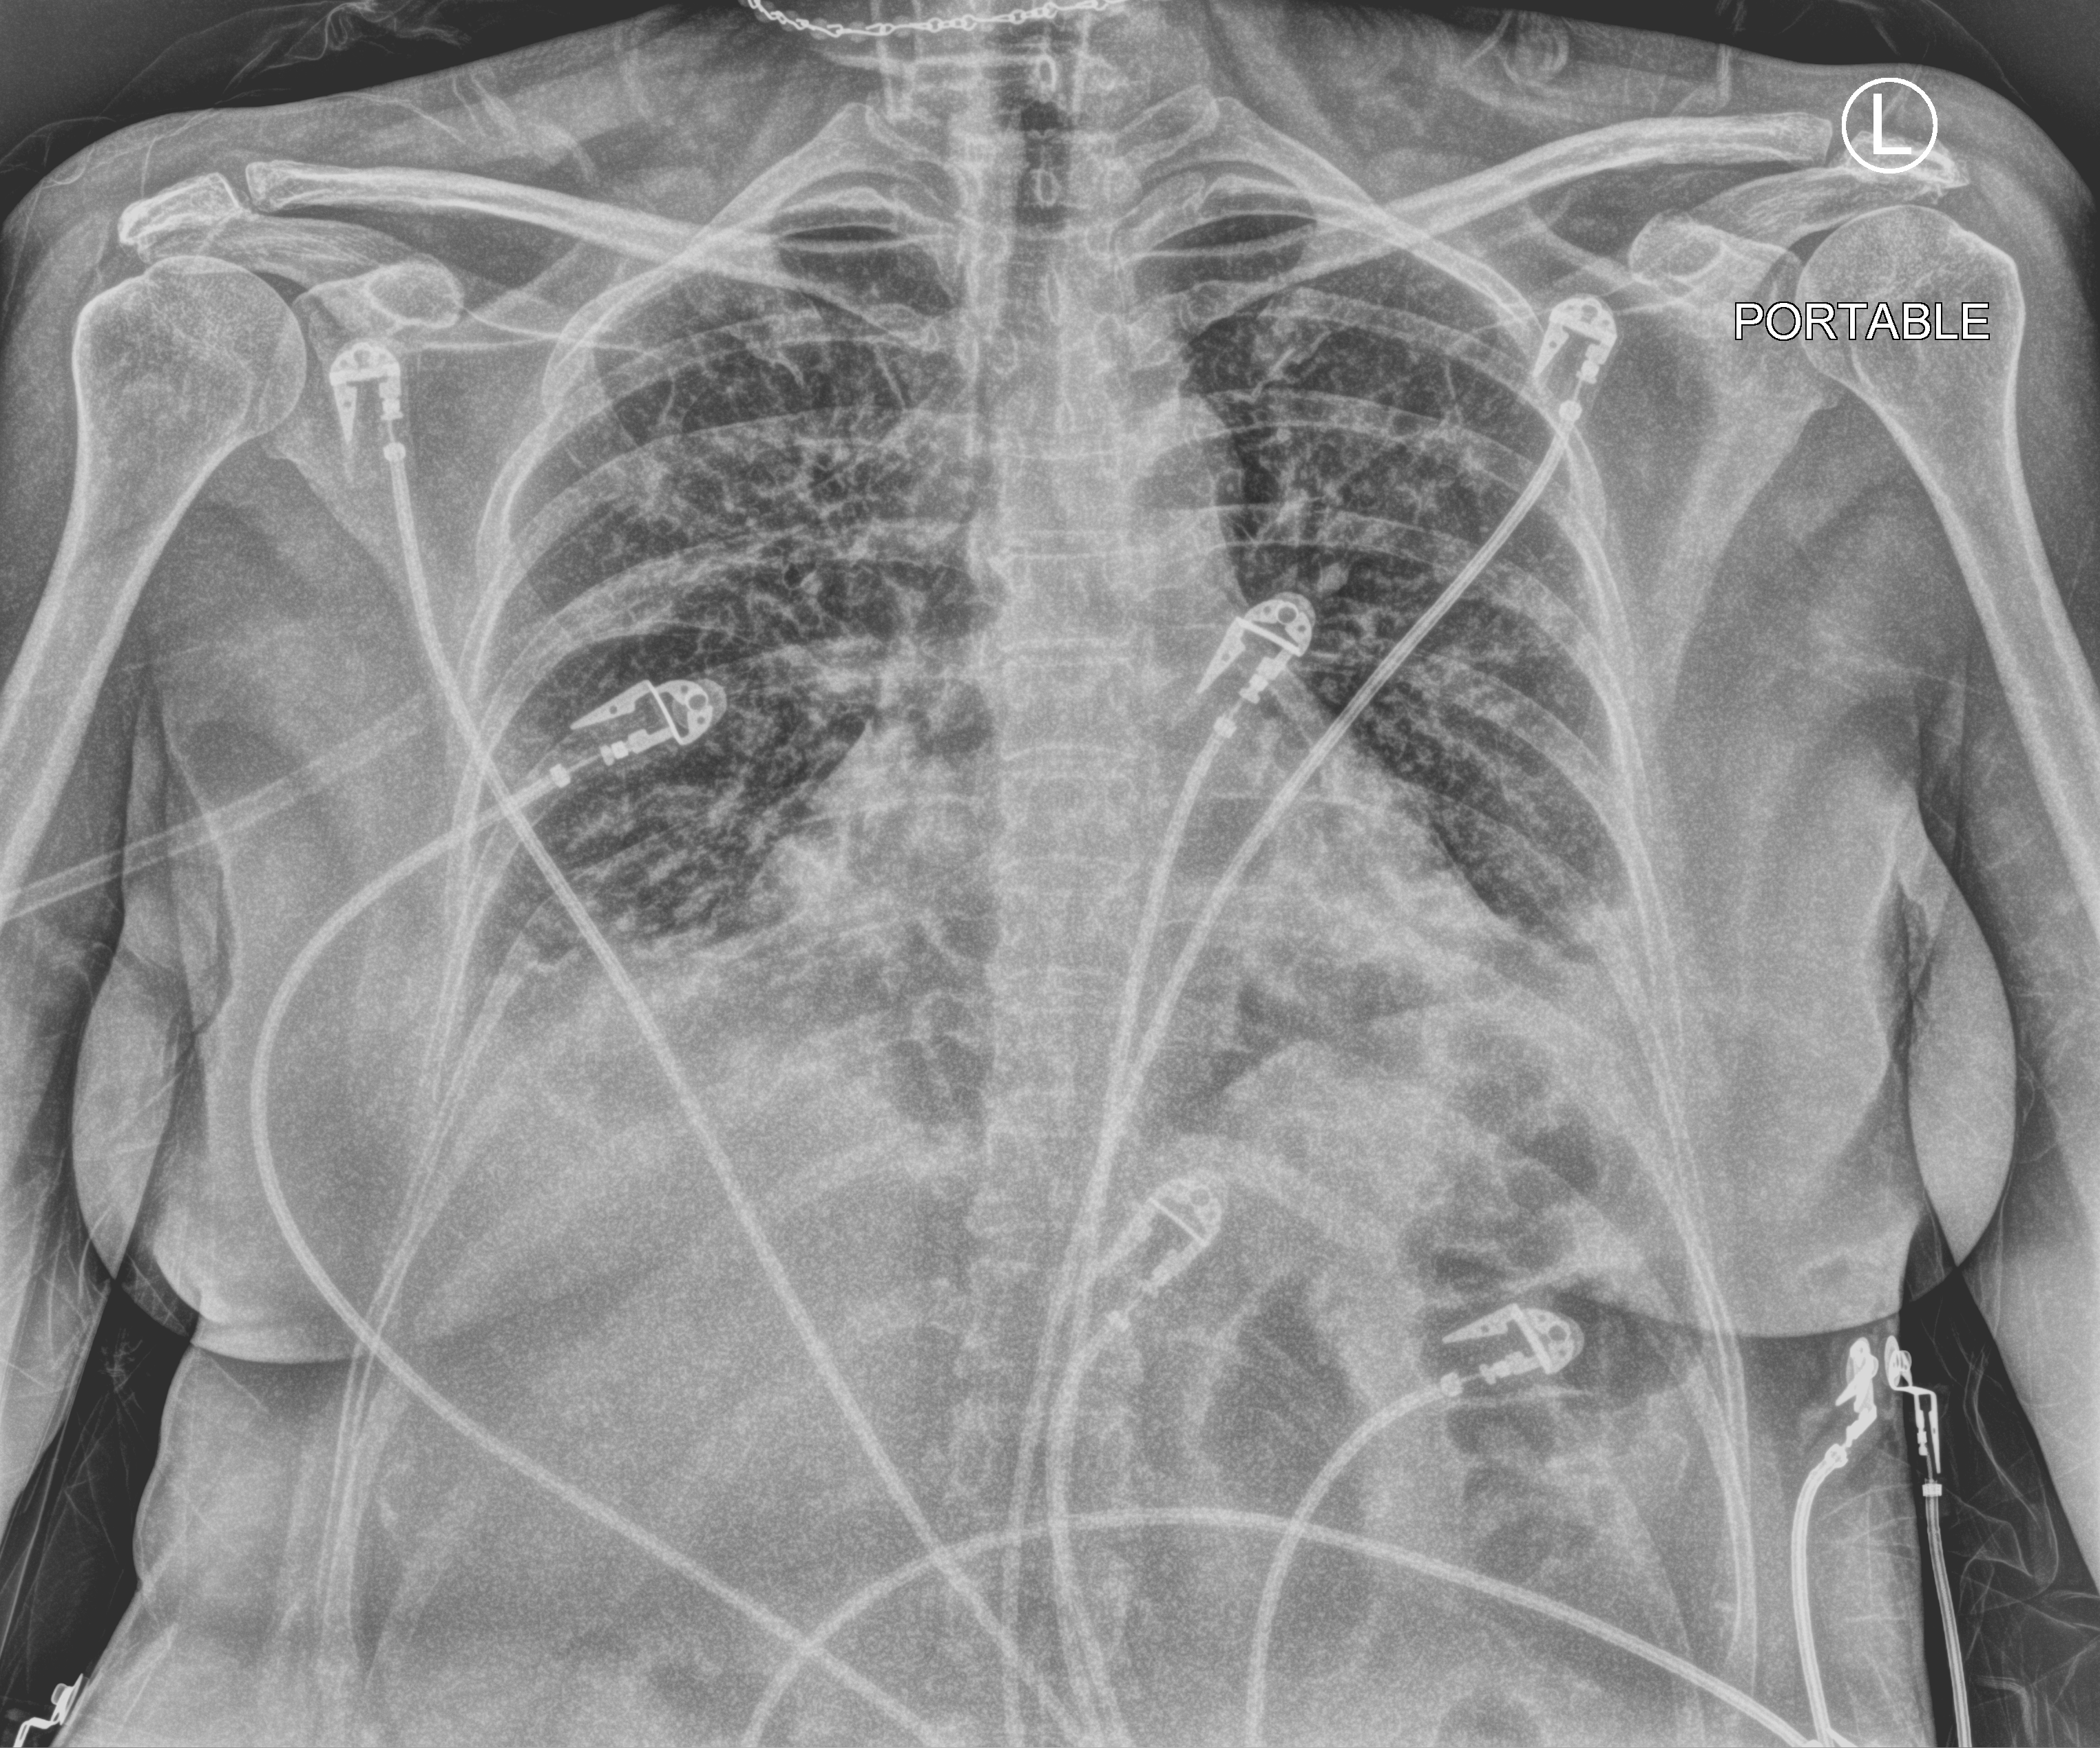
Portable chest radiograph. Female patient hospitalised with COVID-19, age 60–74 years.
Admission-level facts for this patient (not findings on this image; timing relative to this image not recorded): length of hospital stay: 6 days; admitted to intensive care during this hospital stay: no; hypertension (admission record): no.